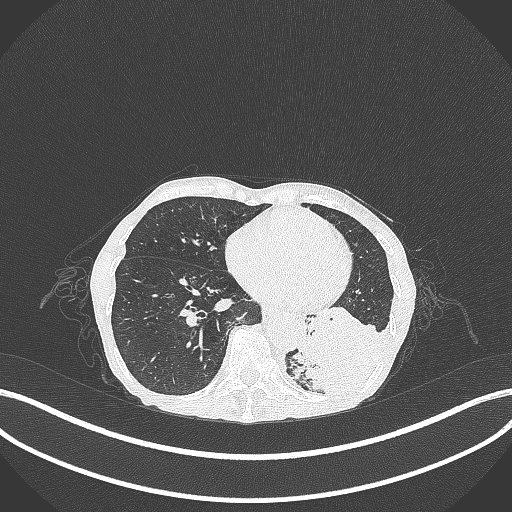
Chest CT, one axial slice; position 86 of 347 along the scan axis; 120 kVp; lung window (W 1500 / L -600 HU); 512 × 512 image matrix. Patient: female, 70 years. From the clinical record (not read from this slice): clinical TNM (as recorded): T3 N0 M0; histopathological grade: G3.
Structures marked on this image (rectangle marked by the reading radiologist):
- lung tumour (recorded histology: small cell carcinoma): bounding box <288,318,392,403> (left, top, right, bottom; pixels)